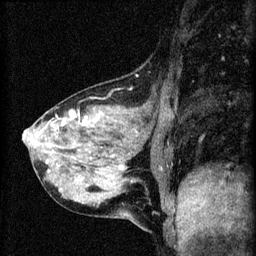
Breast MRI (dynamic contrast-enhanced), one sagittal slice. Slice 20 of 60 in the series (ordered by position). Dynamic contrast-enhanced series, image 2 of 4 at this slice position (ordered by acquisition). 1.5 T. TE 4.2 ms, TR 8.2 ms. 2 mm slice thickness. 256 × 256 image matrix, field of view 180 × 180 mm. Female patient, age 41 years.
Structures marked on this image (semi-automatically segmented with operator editing):
- analysis volume of interest (the breast-tissue region the enhancement analysis was run in; not a lesion): bounding box [x1, y1, x2, y2] px = [23, 93, 166, 208]
- tumour enhancement mask (voxels above the 70 % enhancement threshold inside the analysis volume of interest): [23, 113, 79, 163]